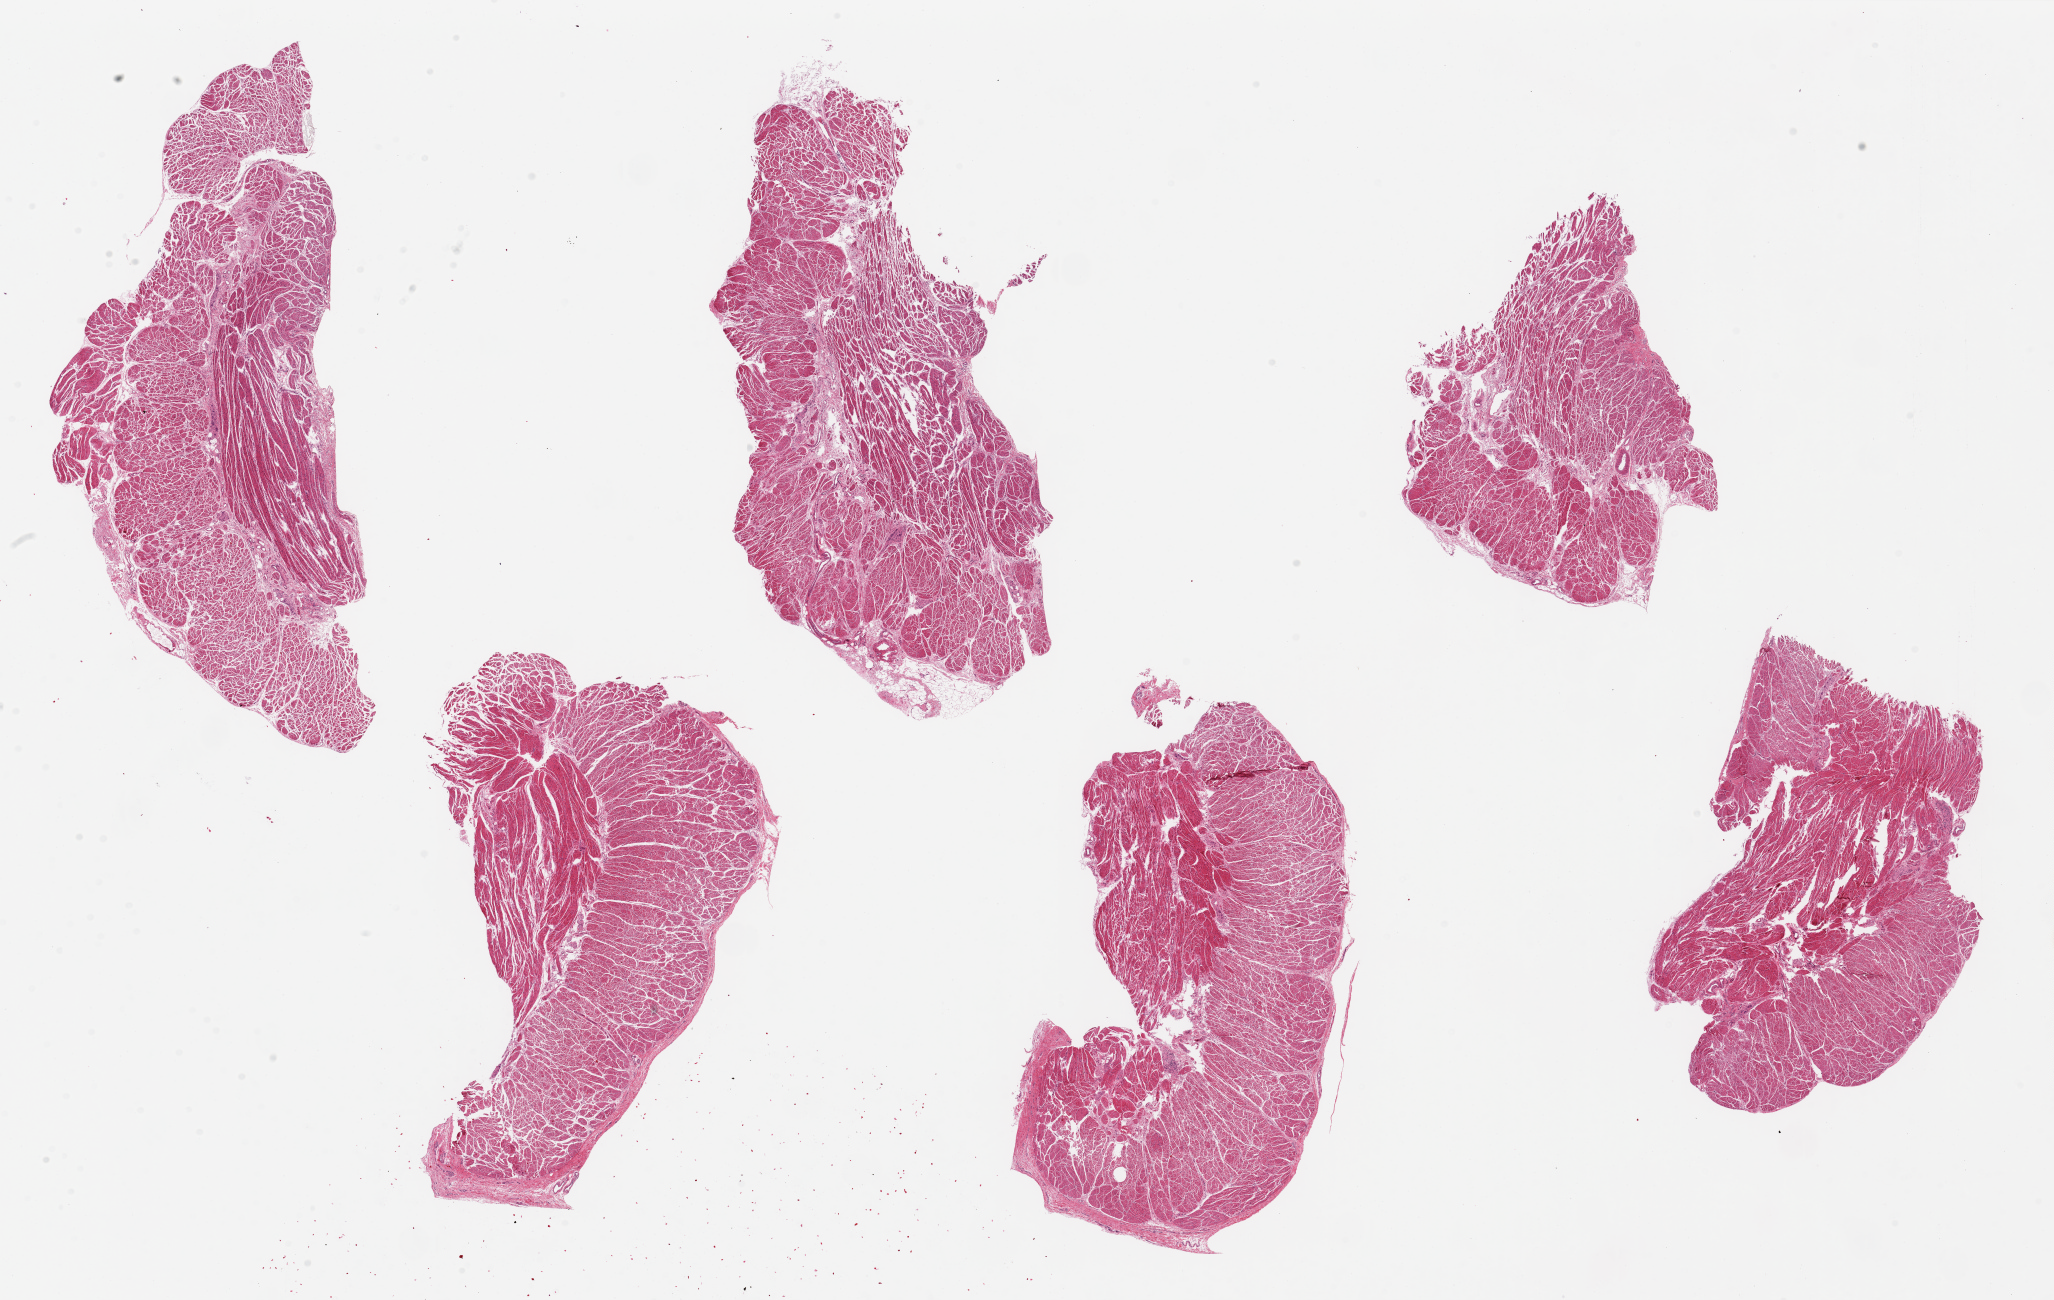
Haematoxylin and eosin whole-slide image — a low-resolution overview of the entire scanned area, about 32.5 x 20.6 mm (slide scanned at 20x), PAXgene-fixed paraffin-embedded (PFPE) section, sampled site (target tissue): esophageal muscle, tissue donor sample. Male donor.
Reviewer comment on this tissue sample: 6 pieces, up to 11x5mm; Well trimmed muscularis.